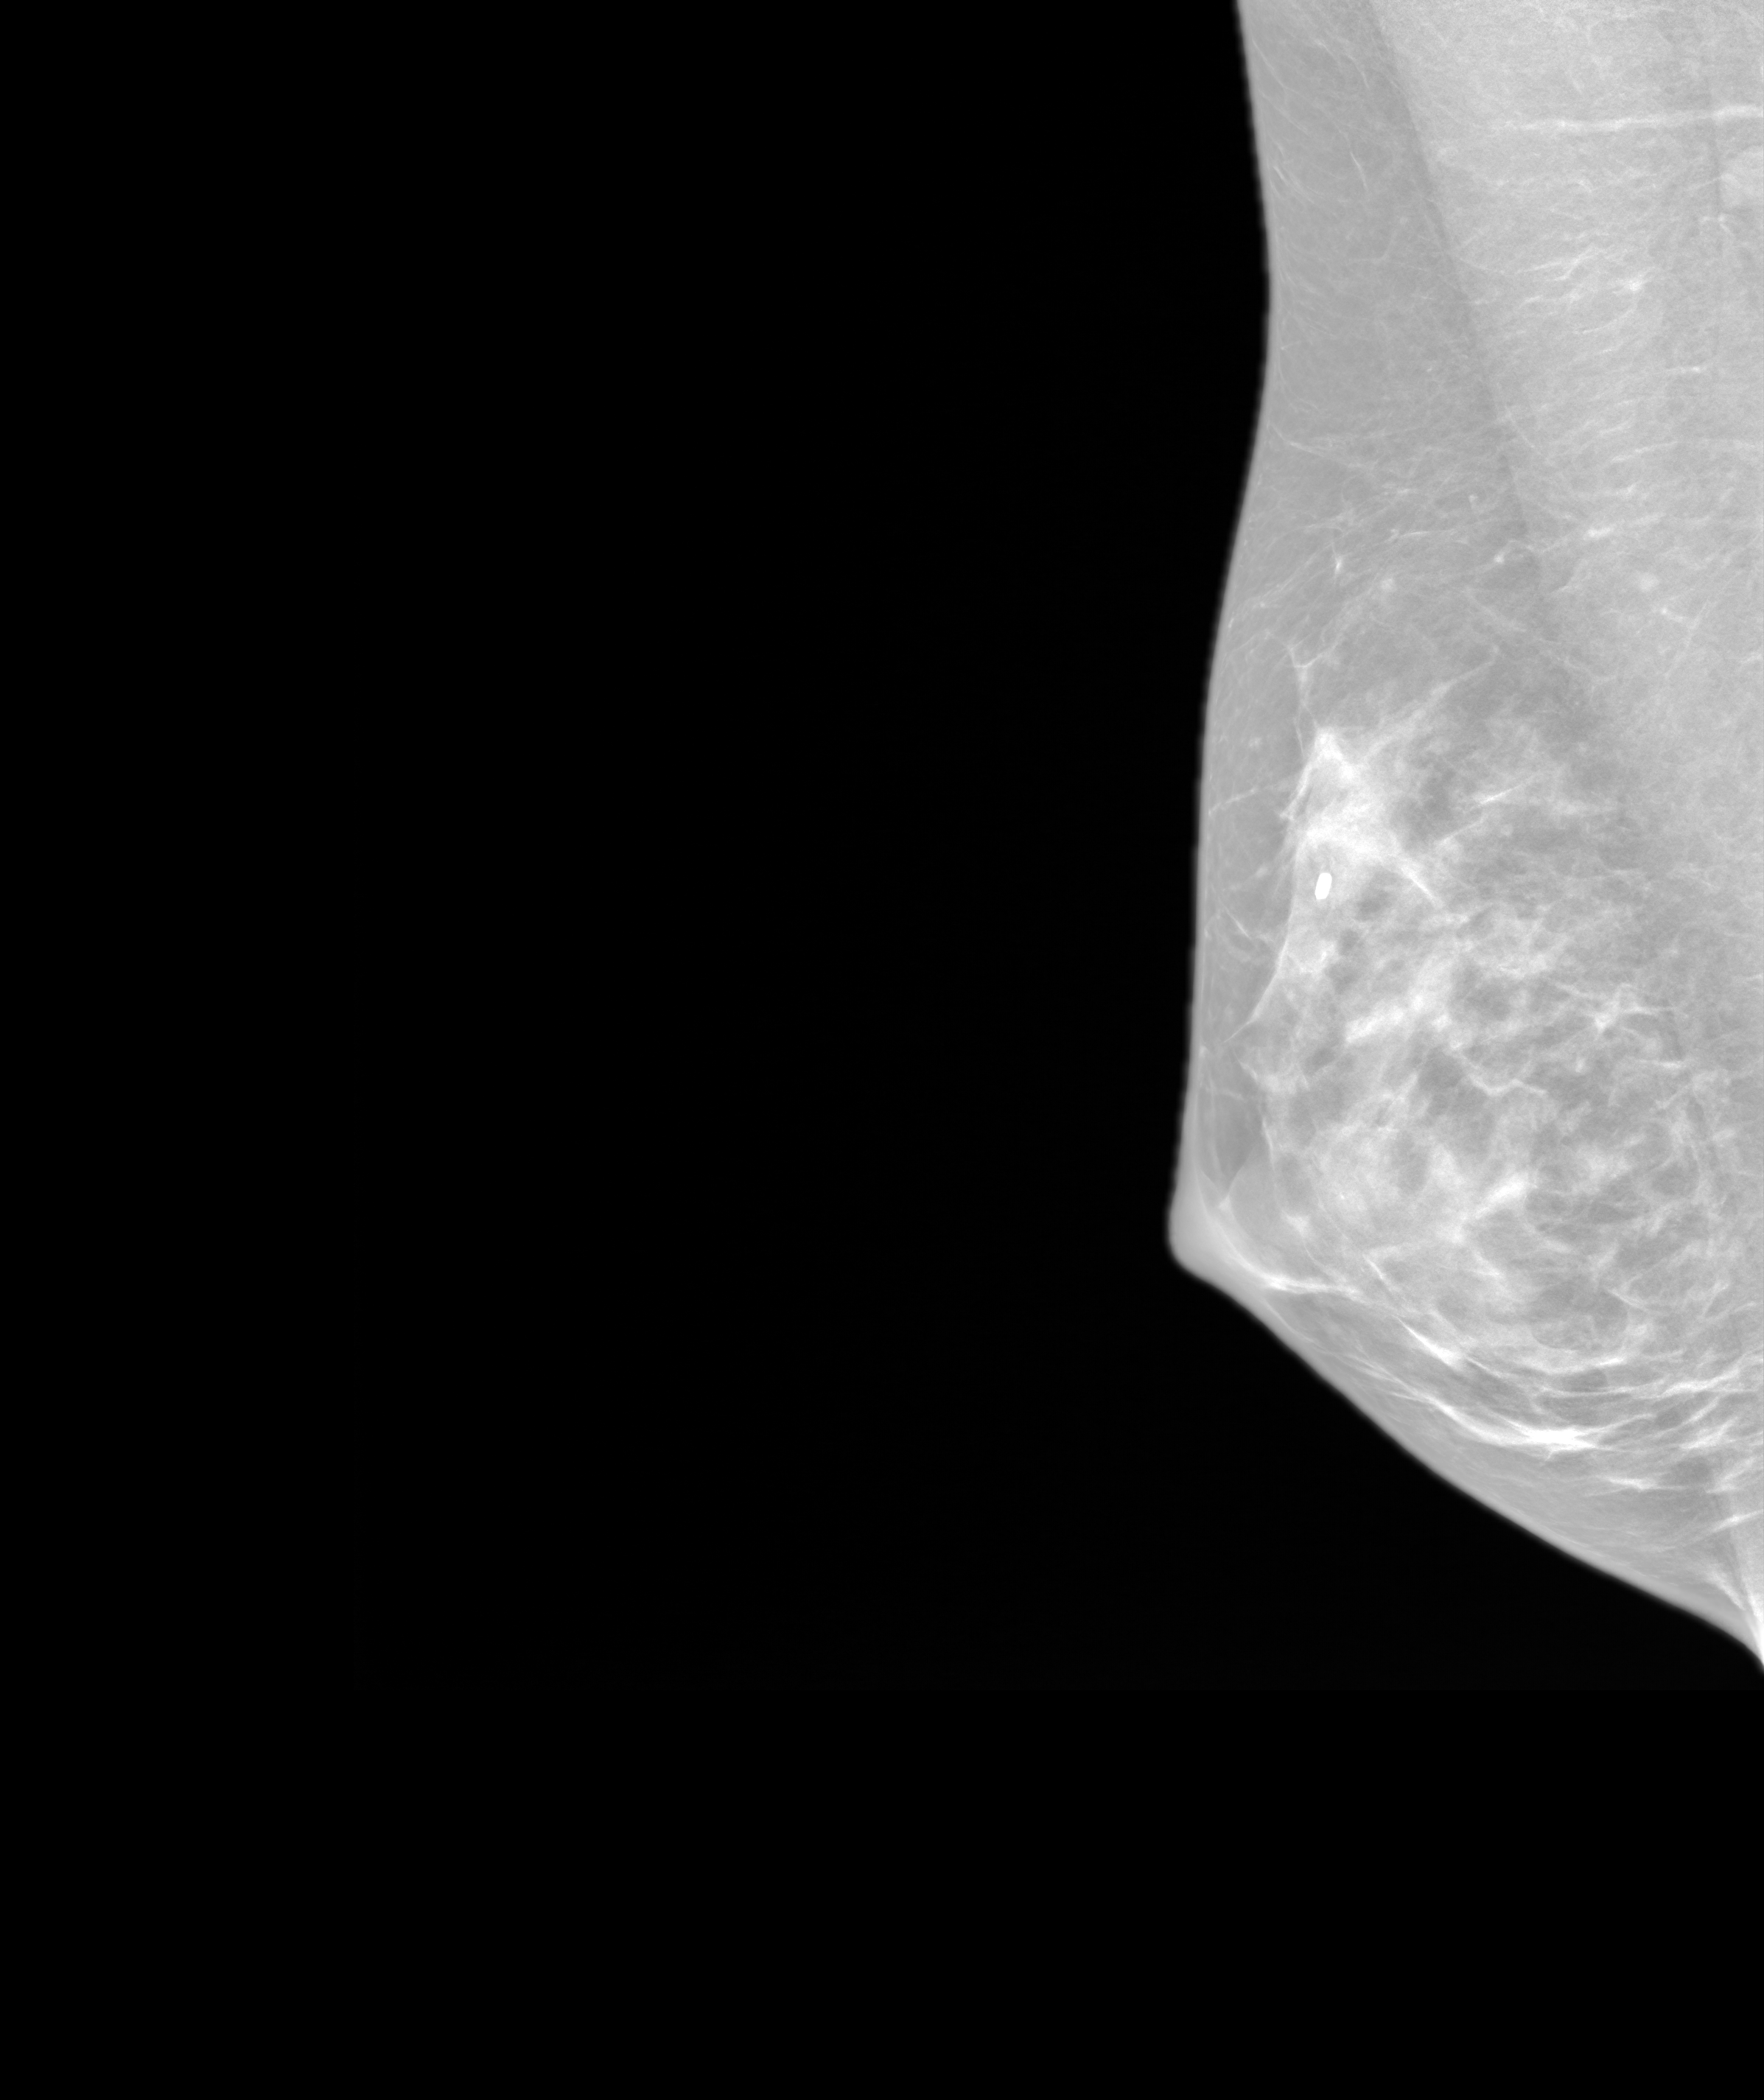
Screening examination; system: SenoIris_1SP2(440). Female patient, age 43 years.
Image type: synthesized 2-D view from tomosynthesis. Breast: right. Projection: MLO view.